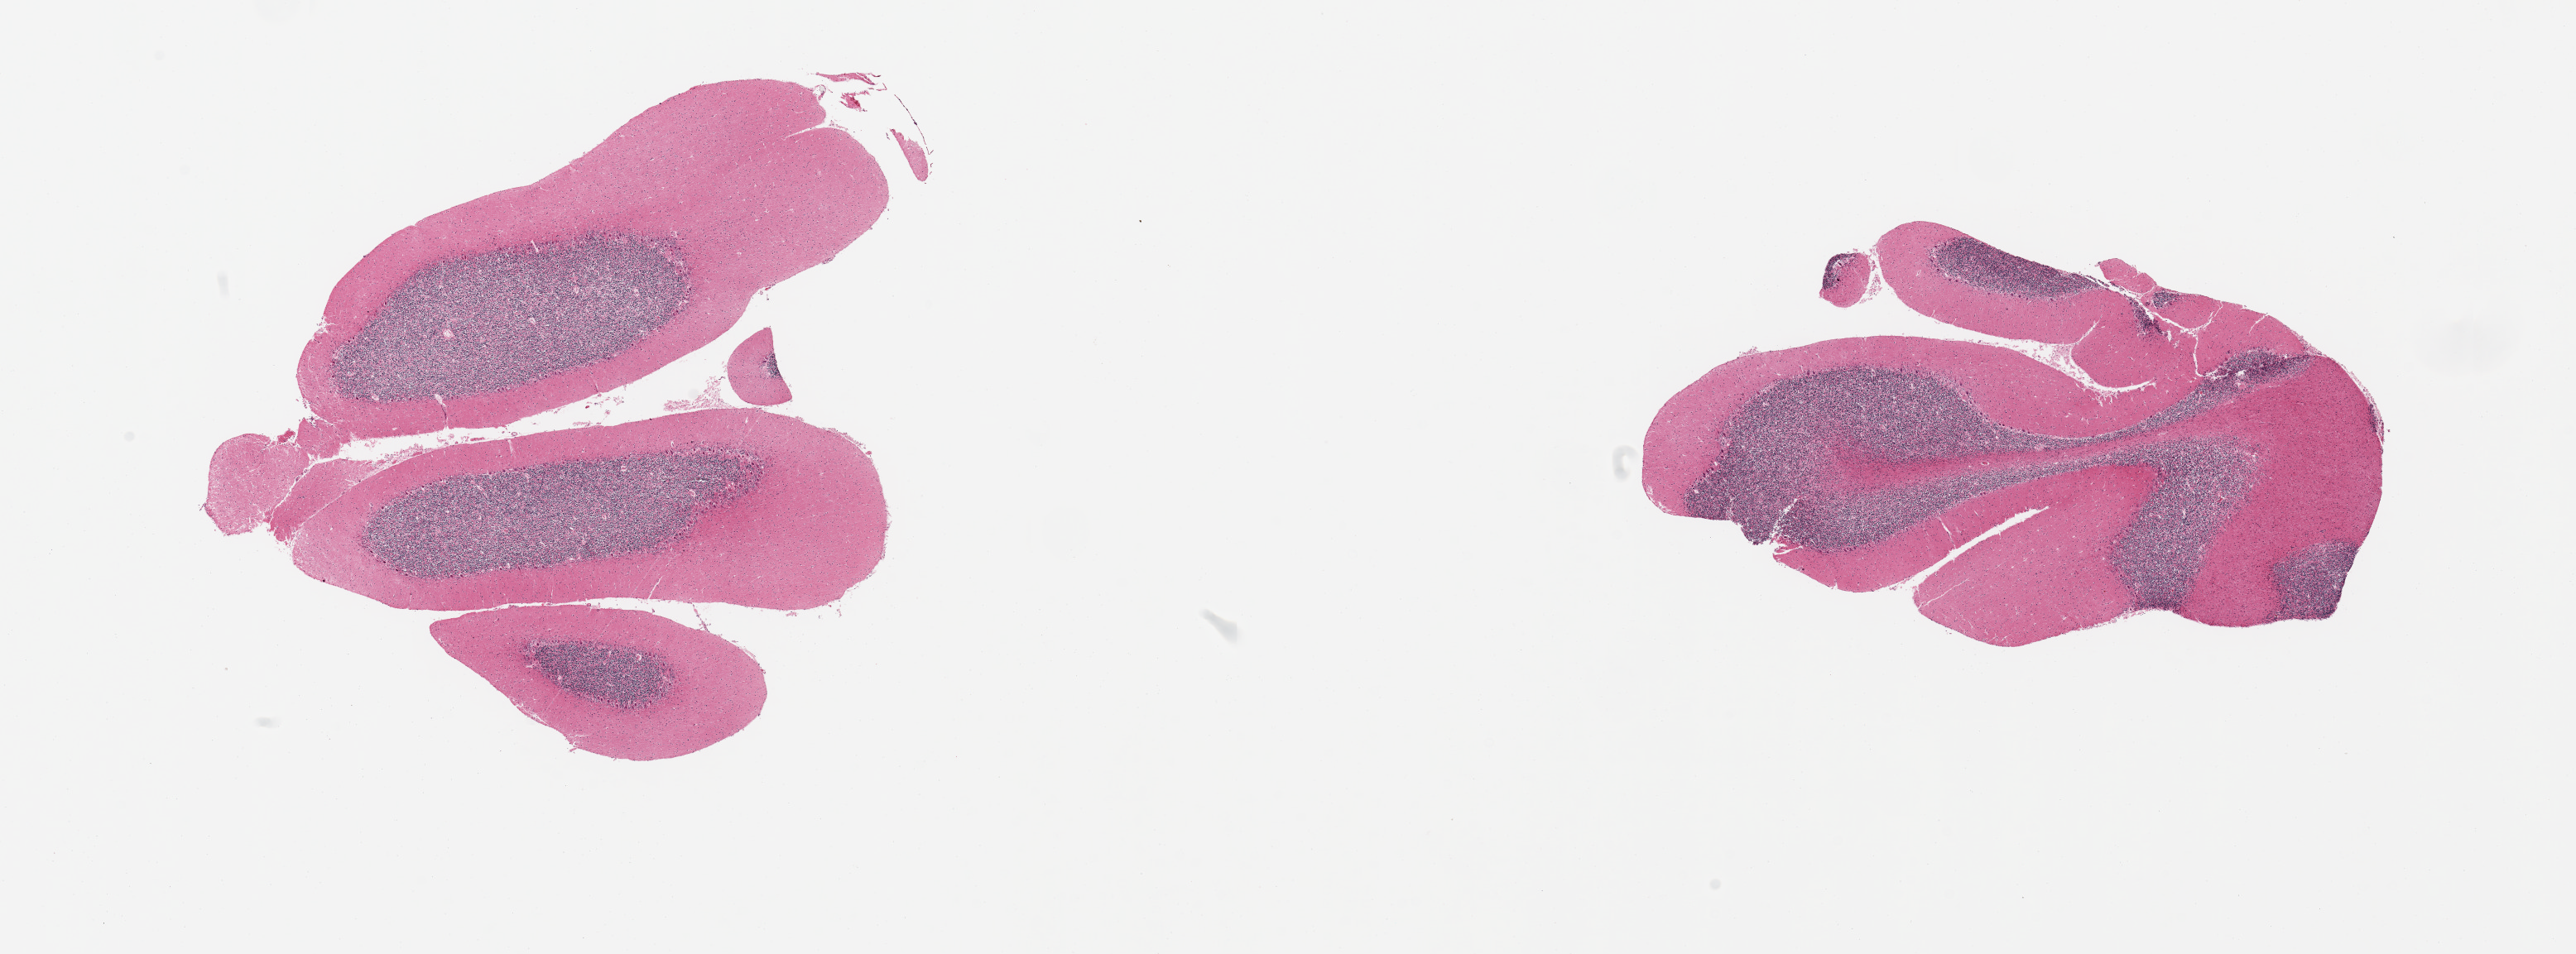
Digitized hematoxylin and eosin (H&E)-stained section, brightfield, low-resolution overview of the scanned area, about 24.6 x 9.1 mm (slide scanned at 20x); PAXgene-fixed paraffin-embedded (PFPE) section; sampled site (target tissue): cerebellum; tissue donor sample. Donor sex: male.
* review note (as recorded): 2 pieces, no abnormalities